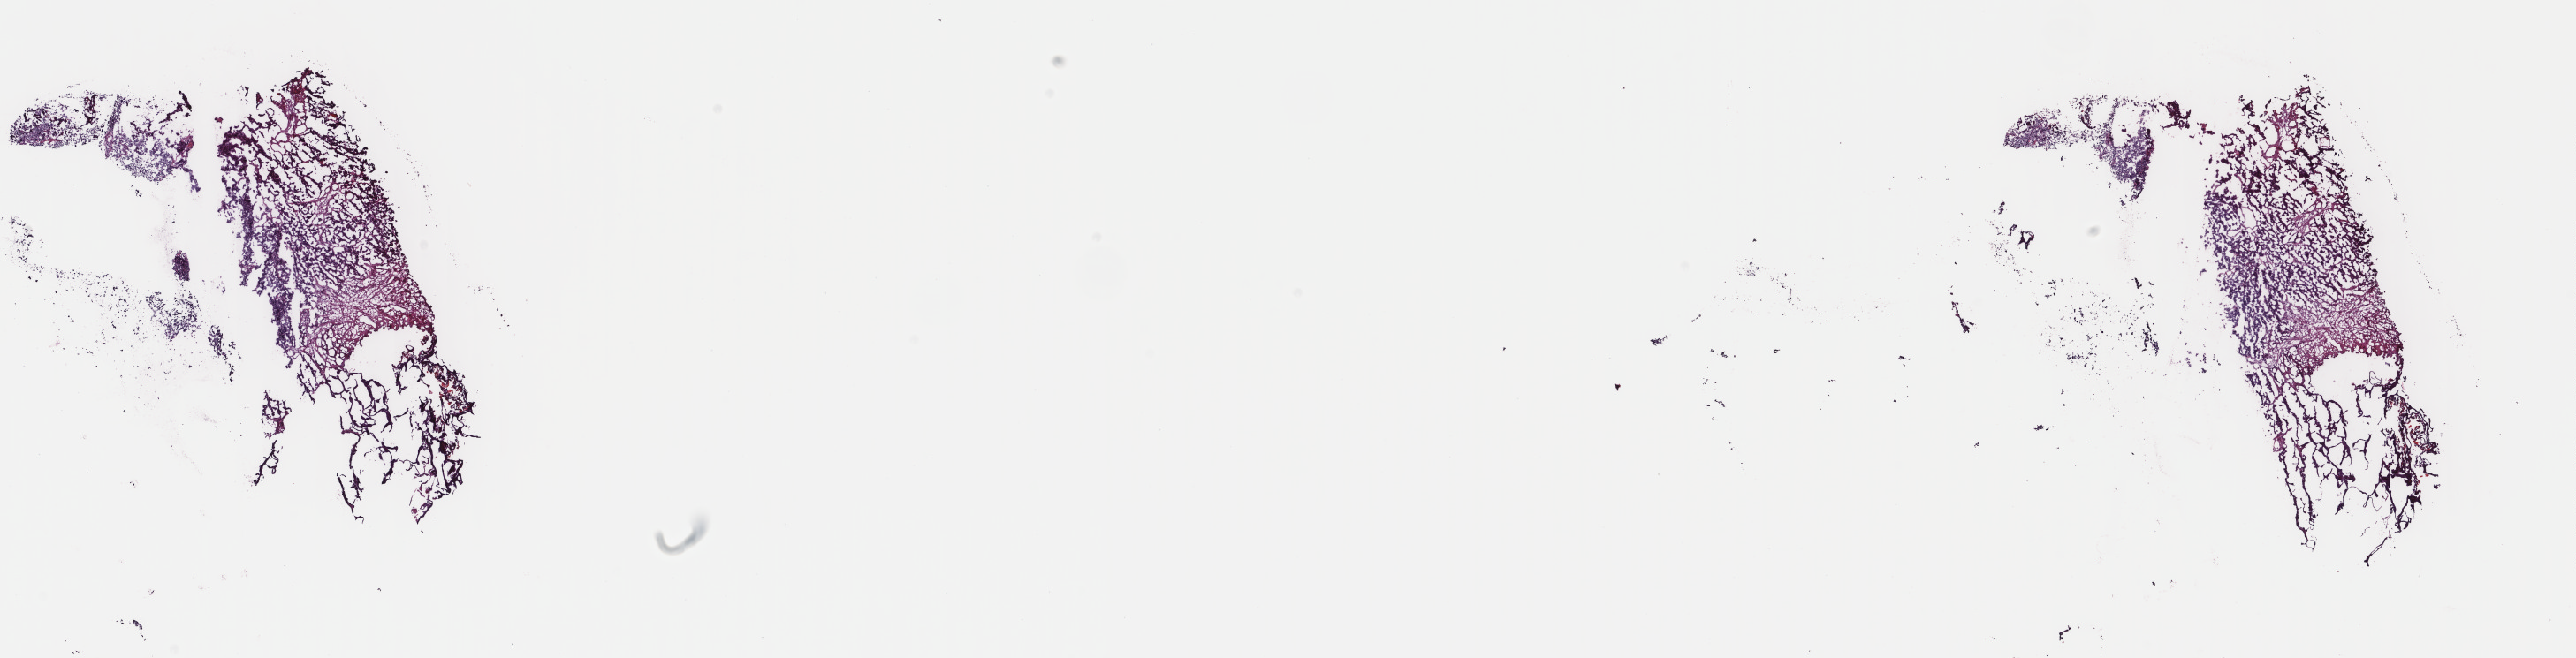
Whole-slide histology image, H&E, low-resolution overview of the scanned area, about 23.1 x 5.9 mm (acquisition: 40x scan). Frozen section from the top of the tissue portion. Primary tumour sample from the bladder. Patient: male, age at initial diagnosis 77 years. Histologic grade: high grade. Pathologist review of this section (percent, as recorded): tumour cells 80%, tumour nuclei 80%, normal cells 0%, stromal cells 20%, necrosis 0%. Infiltration values recorded for this section: lymphocyte infiltration 3%, monocyte infiltration 0%, neutrophil infiltration 0%.
- diagnosis: Transitional cell carcinoma (lateral wall of bladder)
- TNM: N0 M0
- AJCC pathologic stage: II (6th edition)